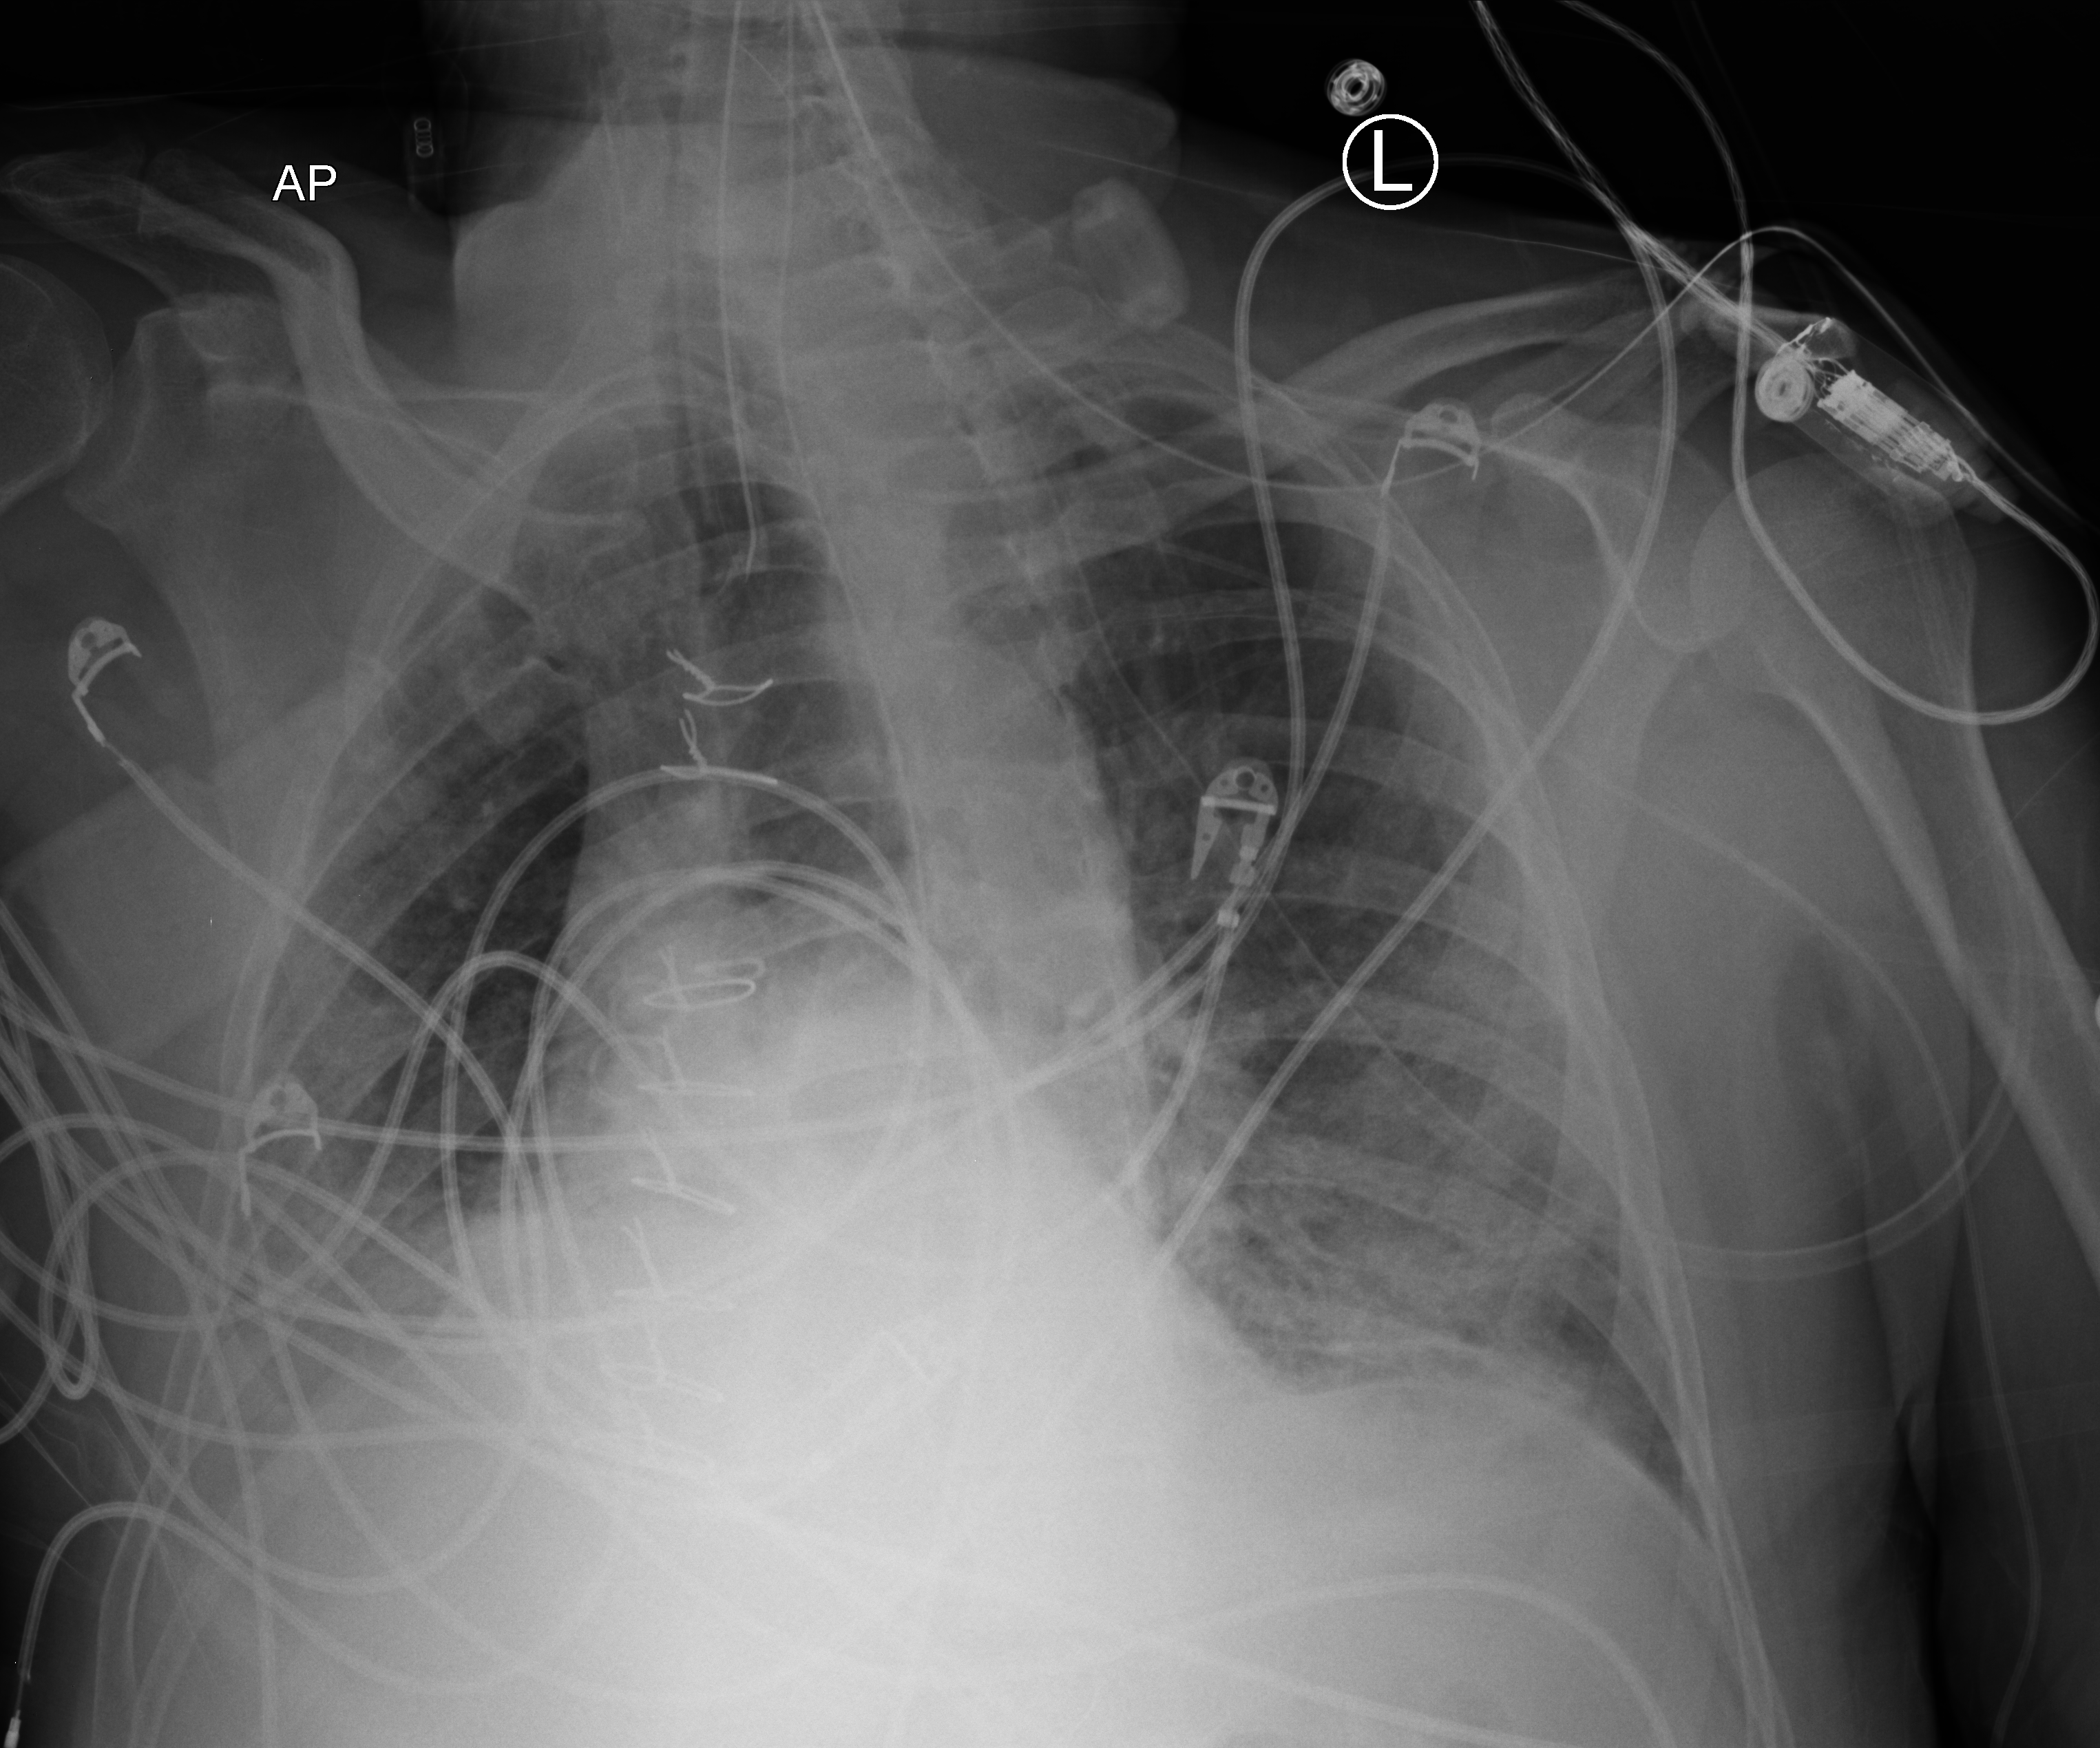
Portable chest radiograph; anteroposterior (AP) projection. Male patient hospitalised with COVID-19, age 18–59 years.
From the hospital-stay record, not from the radiograph (when in the stay this image was taken is not recorded):
- length of hospital stay: 63 days
- hypertension (admission record): no